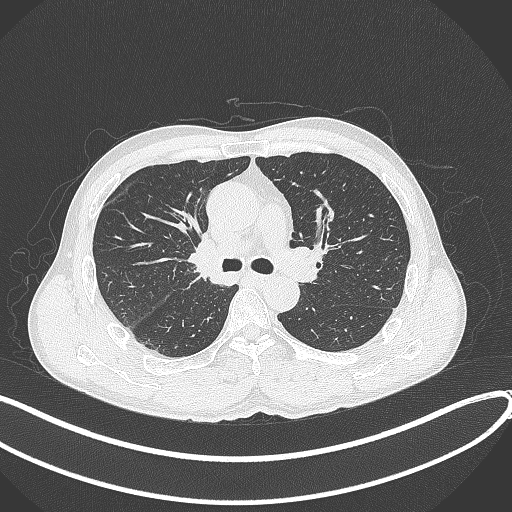
Chest CT, one axial slice; position 241 of 409 along the scan axis; reconstruction kernel B70f; 120 kVp; lung window (W 1500 / L -600 HU); 512 × 512 image matrix. Male patient, age 53 years. From the clinical record (not read from this slice): clinical TNM (as recorded): T1b N0 M0.
Annotated regions visible in this slice (bounding box drawn by a radiologist):
- lung tumour (recorded histology: squamous cell carcinoma): box from (x=182, y=233) to (x=222, y=285) px